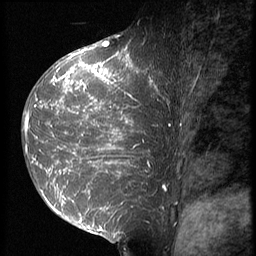
Breast MRI (dynamic contrast-enhanced), one sagittal slice. Position 35 of 64 along the scan axis. 3 images stored at this slice position (order not interpretable as contrast timing). 1.5 T. TE 4.2 ms, TR 9 ms. 2.5 mm slice thickness. 256 × 256 image matrix, field of view 180 × 180 mm. Patient: female, 39 years. Case-level facts recorded for this patient, not image findings: setting: breast cancer imaged before/during neoadjuvant chemotherapy; receptor status: HER2-positive.
Outlined on this slice (semi-automatic segmentation, software-assisted and operator-edited):
- analysis volume of interest (the breast-tissue region the enhancement analysis was run in; not a lesion): bounding box <23,47,165,239> (left, top, right, bottom; pixels)
- tumour enhancement mask (voxels above the 140 % enhancement threshold inside the analysis volume of interest): <24,47,164,228>